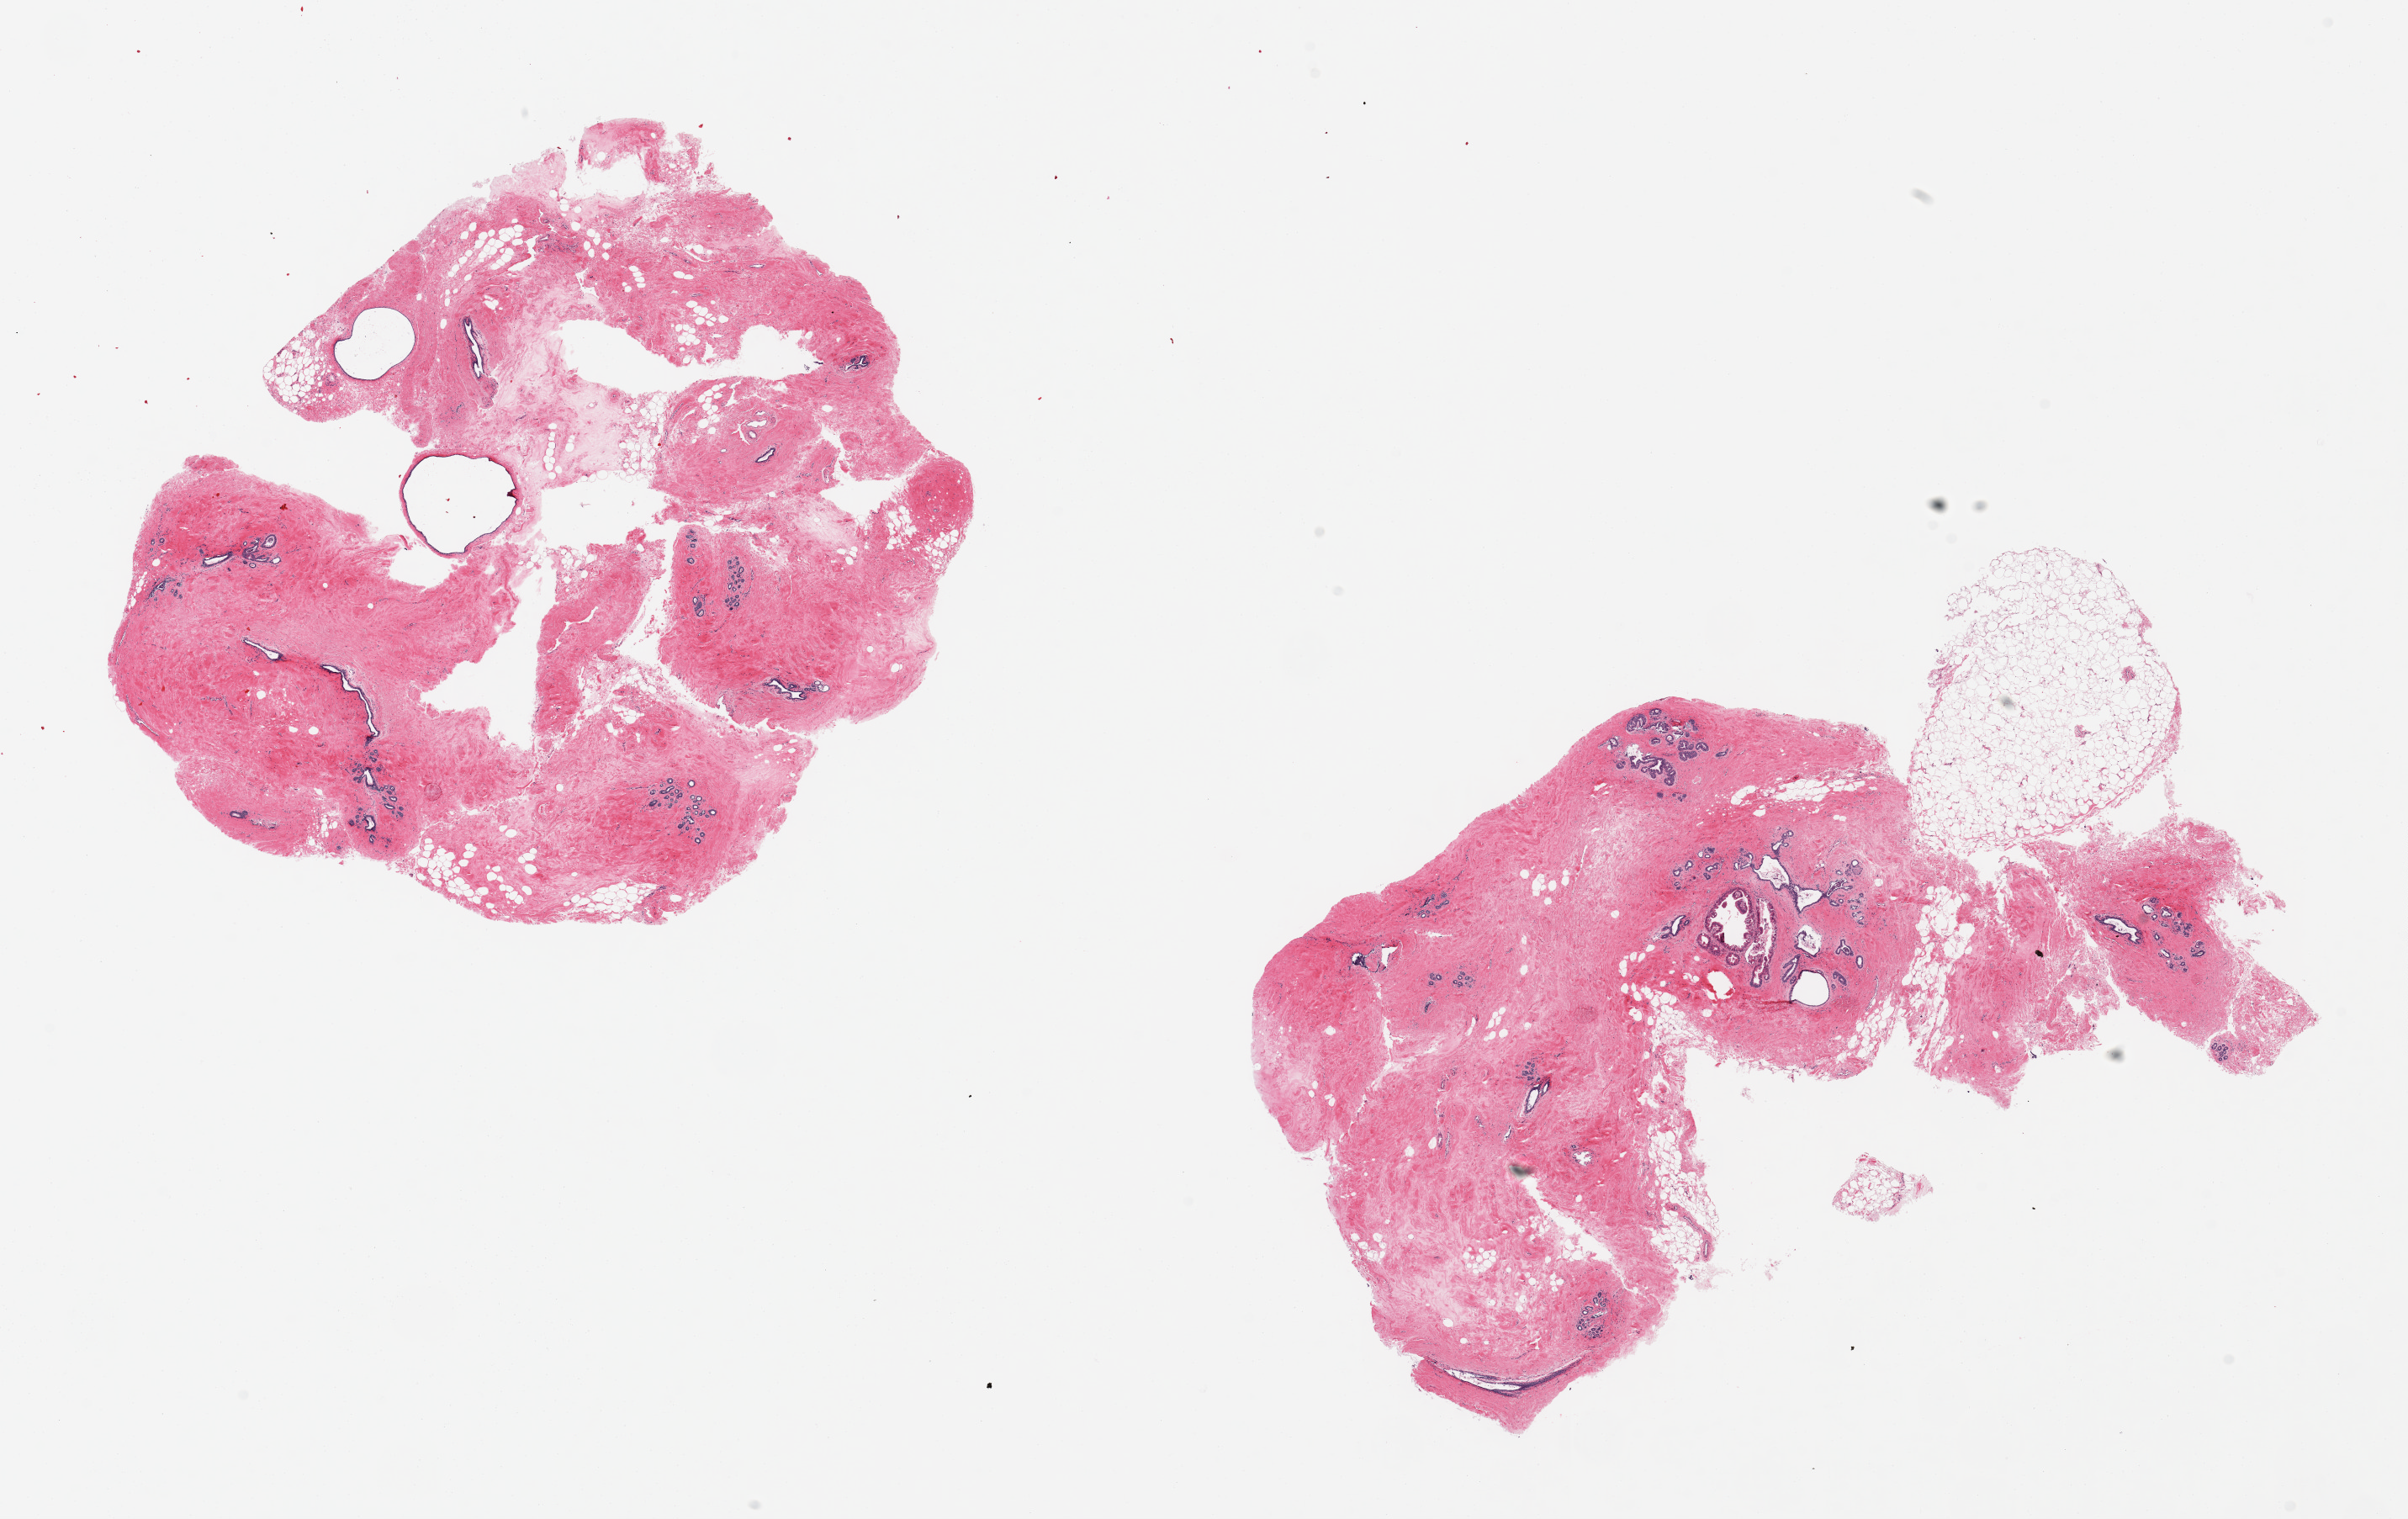
Hematoxylin and eosin (H&E) whole-slide image, low-resolution overview of the scanned area, about 22.6 x 14.3 mm (from a 20x scan), PAXgene-fixed paraffin-embedded (PFPE) section, target tissue: breast, donor tissue sample. Donor: female.
- review note (as recorded): 2 pieces; fibrocystic changes